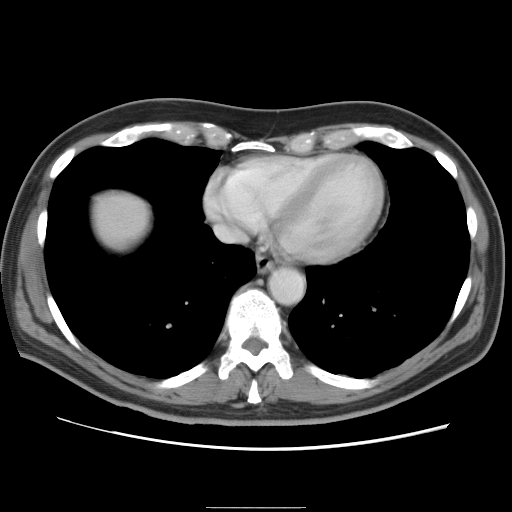
Contrast-enhanced abdominal CT, one axial slice; slice 82 of 87 in the series (ordered by position); 120 kVp; intravenous contrast given; soft-tissue window (W 400 / L 40 HU); 5 mm slice thickness; 512 × 512 image matrix, field of view 363 × 363 mm. Male patient, age 63 years. From the clinical record (not read from this slice): diagnosis: colorectal cancer liver metastases, imaged before liver resection; multiple liver metastases: no; largest metastasis: 9 cm.
Structures marked on this image (outlined manually by an expert reader):
- liver: bounding box <97,195,146,240> (left, top, right, bottom; pixels)
- planned liver remnant (the part of the liver to remain after resection): <99,197,146,238>